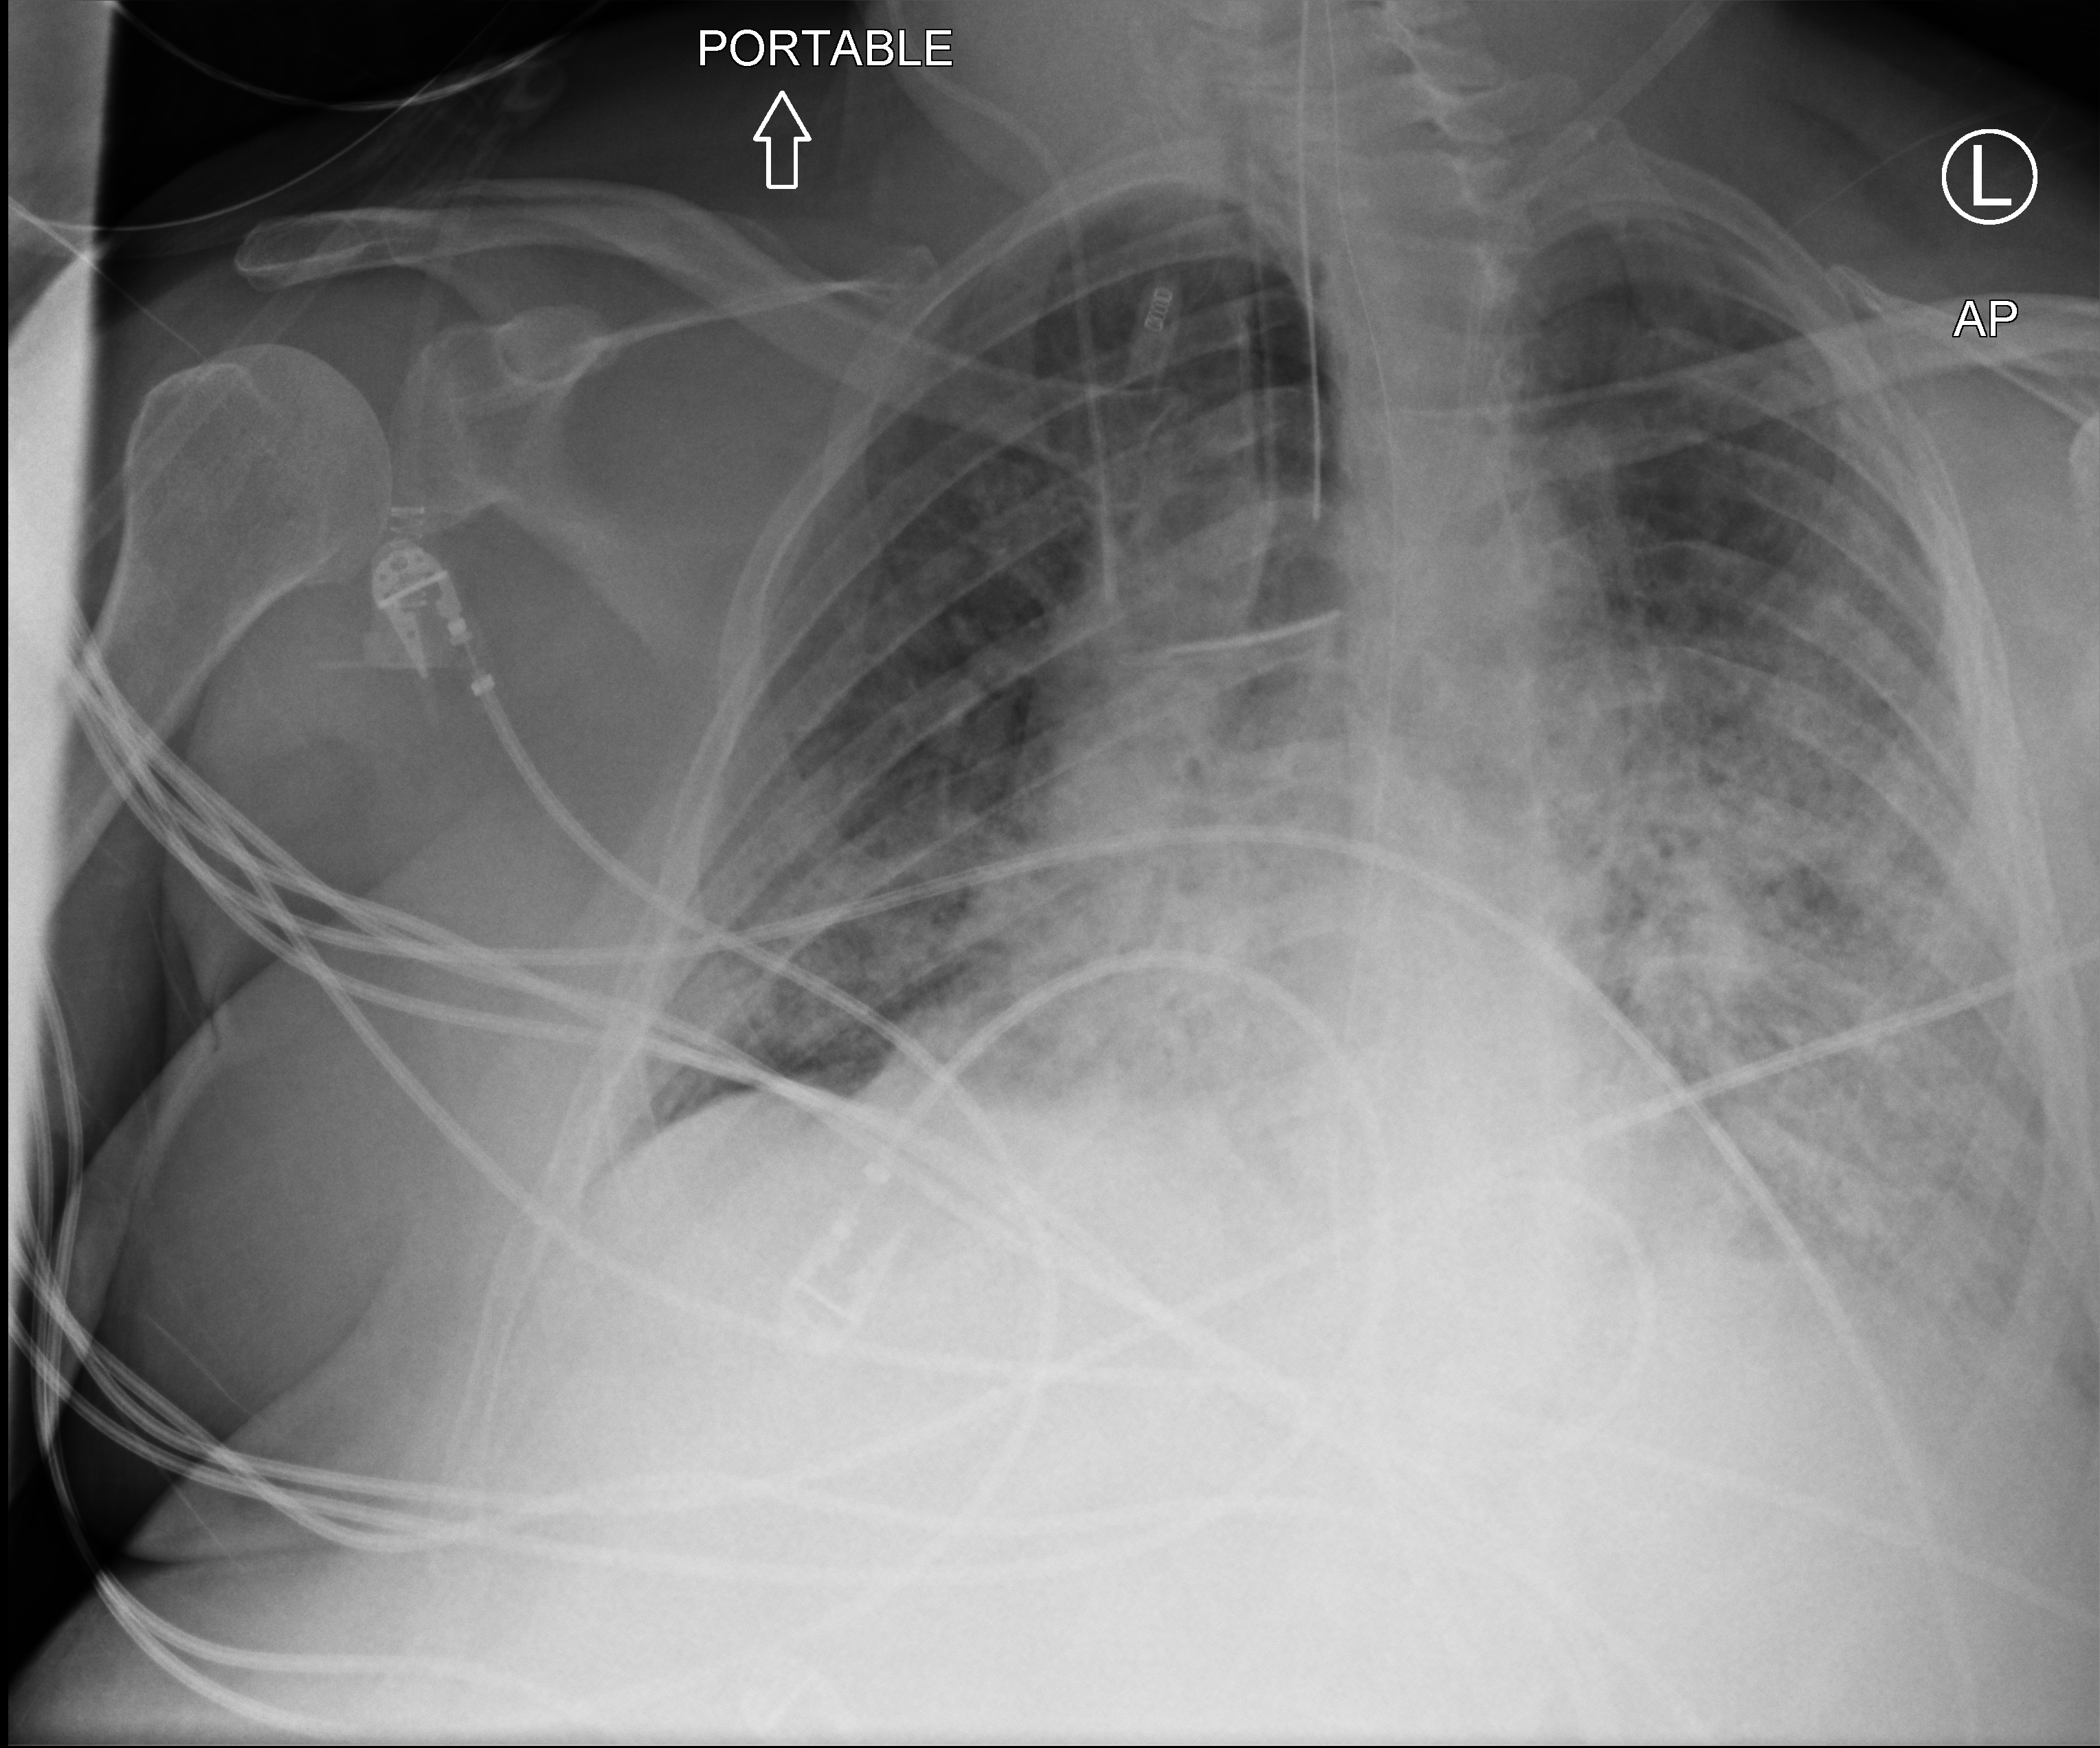
Chest X-ray (portable); anteroposterior (AP) projection. Patient hospitalised with COVID-19; male, aged 18–59 years.
From the hospital-stay record, not from the radiograph (when in the stay this image was taken is not recorded):
- diabetes (admission record): no
- length of hospital stay: 39 days